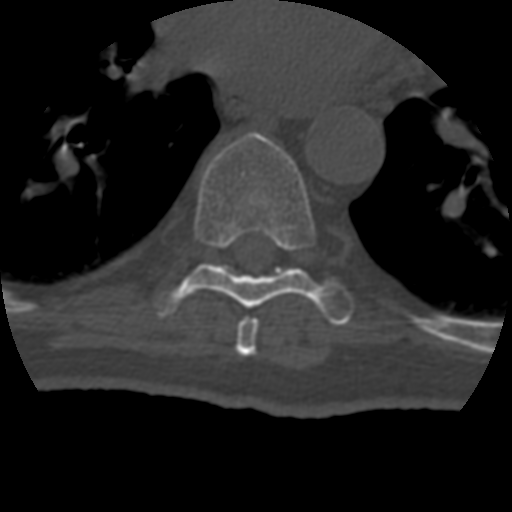
CT including the spine, one axial slice; position 259 of 399 along the scan axis; bone window (W 1800 / L 400 HU); 512 × 512 image matrix, field of view 160 × 160 mm. Patient age 69 years. From the clinical record (not read from this slice): primary cancer: prostate.
Structures marked on this image (semi-automatically segmented with operator editing):
- T7 vertebra: bounding box (x1, y1, x2, y2) in pixels: (235, 317, 259, 356)
- T8 vertebra: (155, 132, 354, 325)